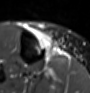
MRI of an extremity soft-tissue mass, one axial slice. Slice 21 of 60 in the series (ordered by position). STIR. MR volume resampled by the dataset authors to the PET/CT grid (not the native acquisition matrix). 3.27 mm slice thickness. 90 × 93 image matrix, field of view 88 × 91 mm. Female patient. From the clinical record (not read from this slice): histological type: undifferentiated – high grade; grade: high; site of the primary tumour: right thigh.
Structures marked on this image (expert contour drawn on MRI and transferred to this co-registered scan by the dataset authors):
- gross tumour volume (mass): bounding box (x1, y1, x2, y2) in pixels: (35, 30, 59, 59)